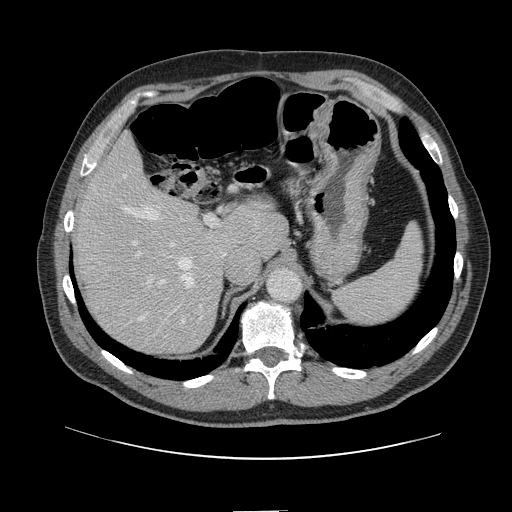
Contrast-enhanced abdominal CT, one axial slice; slice 96 of 161 in the series (ordered by position); 120 kVp; intravenous contrast given; soft-tissue window (W 400 / L 40 HU); 2.5 mm slice thickness; 512 × 512 image matrix, field of view 412 × 412 mm. Male patient, age 66 years. Case-level facts recorded for this patient, not image findings: diagnosis: colorectal cancer liver metastases, imaged before liver resection; multiple liver metastases: no; largest metastasis: 3.5 cm; disease in both lobes: no.
Structures marked on this image (expert manual segmentation):
- hepatic veins: bounding box <121,176,194,321> (left, top, right, bottom; pixels)
- liver: <80,140,286,353>
- planned liver remnant (the part of the liver to remain after resection): <80,138,286,305>
- portal vein (with intrahepatic branches): <131,213,217,314>